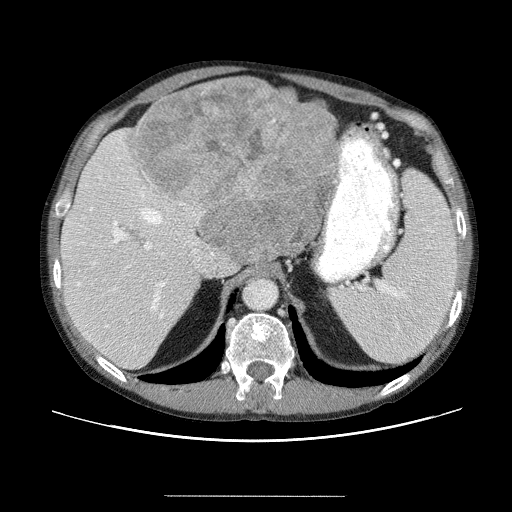
Contrast-enhanced abdominal CT (liver protocol), one axial slice; position 36 of 69 along the scan axis; reconstruction kernel STANDARD; 120 kVp; soft-tissue window (W 400 / L 40 HU); 2.5 mm slice thickness; 512 × 512 image matrix, field of view 380 × 380 mm. From the clinical record (not read from this slice): diagnosis: hepatocellular carcinoma (patient treated with transarterial chemoembolisation; whether this scan precedes or follows treatment is not stated here); TNM stage (as recorded): Stage-IVB; Child-Pugh class: B; tumour differentiation: poorly differentiated; tumour nodularity: multinodular.
Annotated regions visible in this slice (semi-automatic segmentation, software-assisted and operator-edited):
- abdominal aorta: box from (x=244, y=278) to (x=276, y=308) px
- liver parenchyma outside the tumour (the mass and vessels are separate outlines, so this box may not span the whole liver): (x=60, y=86)–(x=332, y=370)
- mass: (x=135, y=76)–(x=339, y=258)
- liver vessels: (x=81, y=159)–(x=211, y=350)